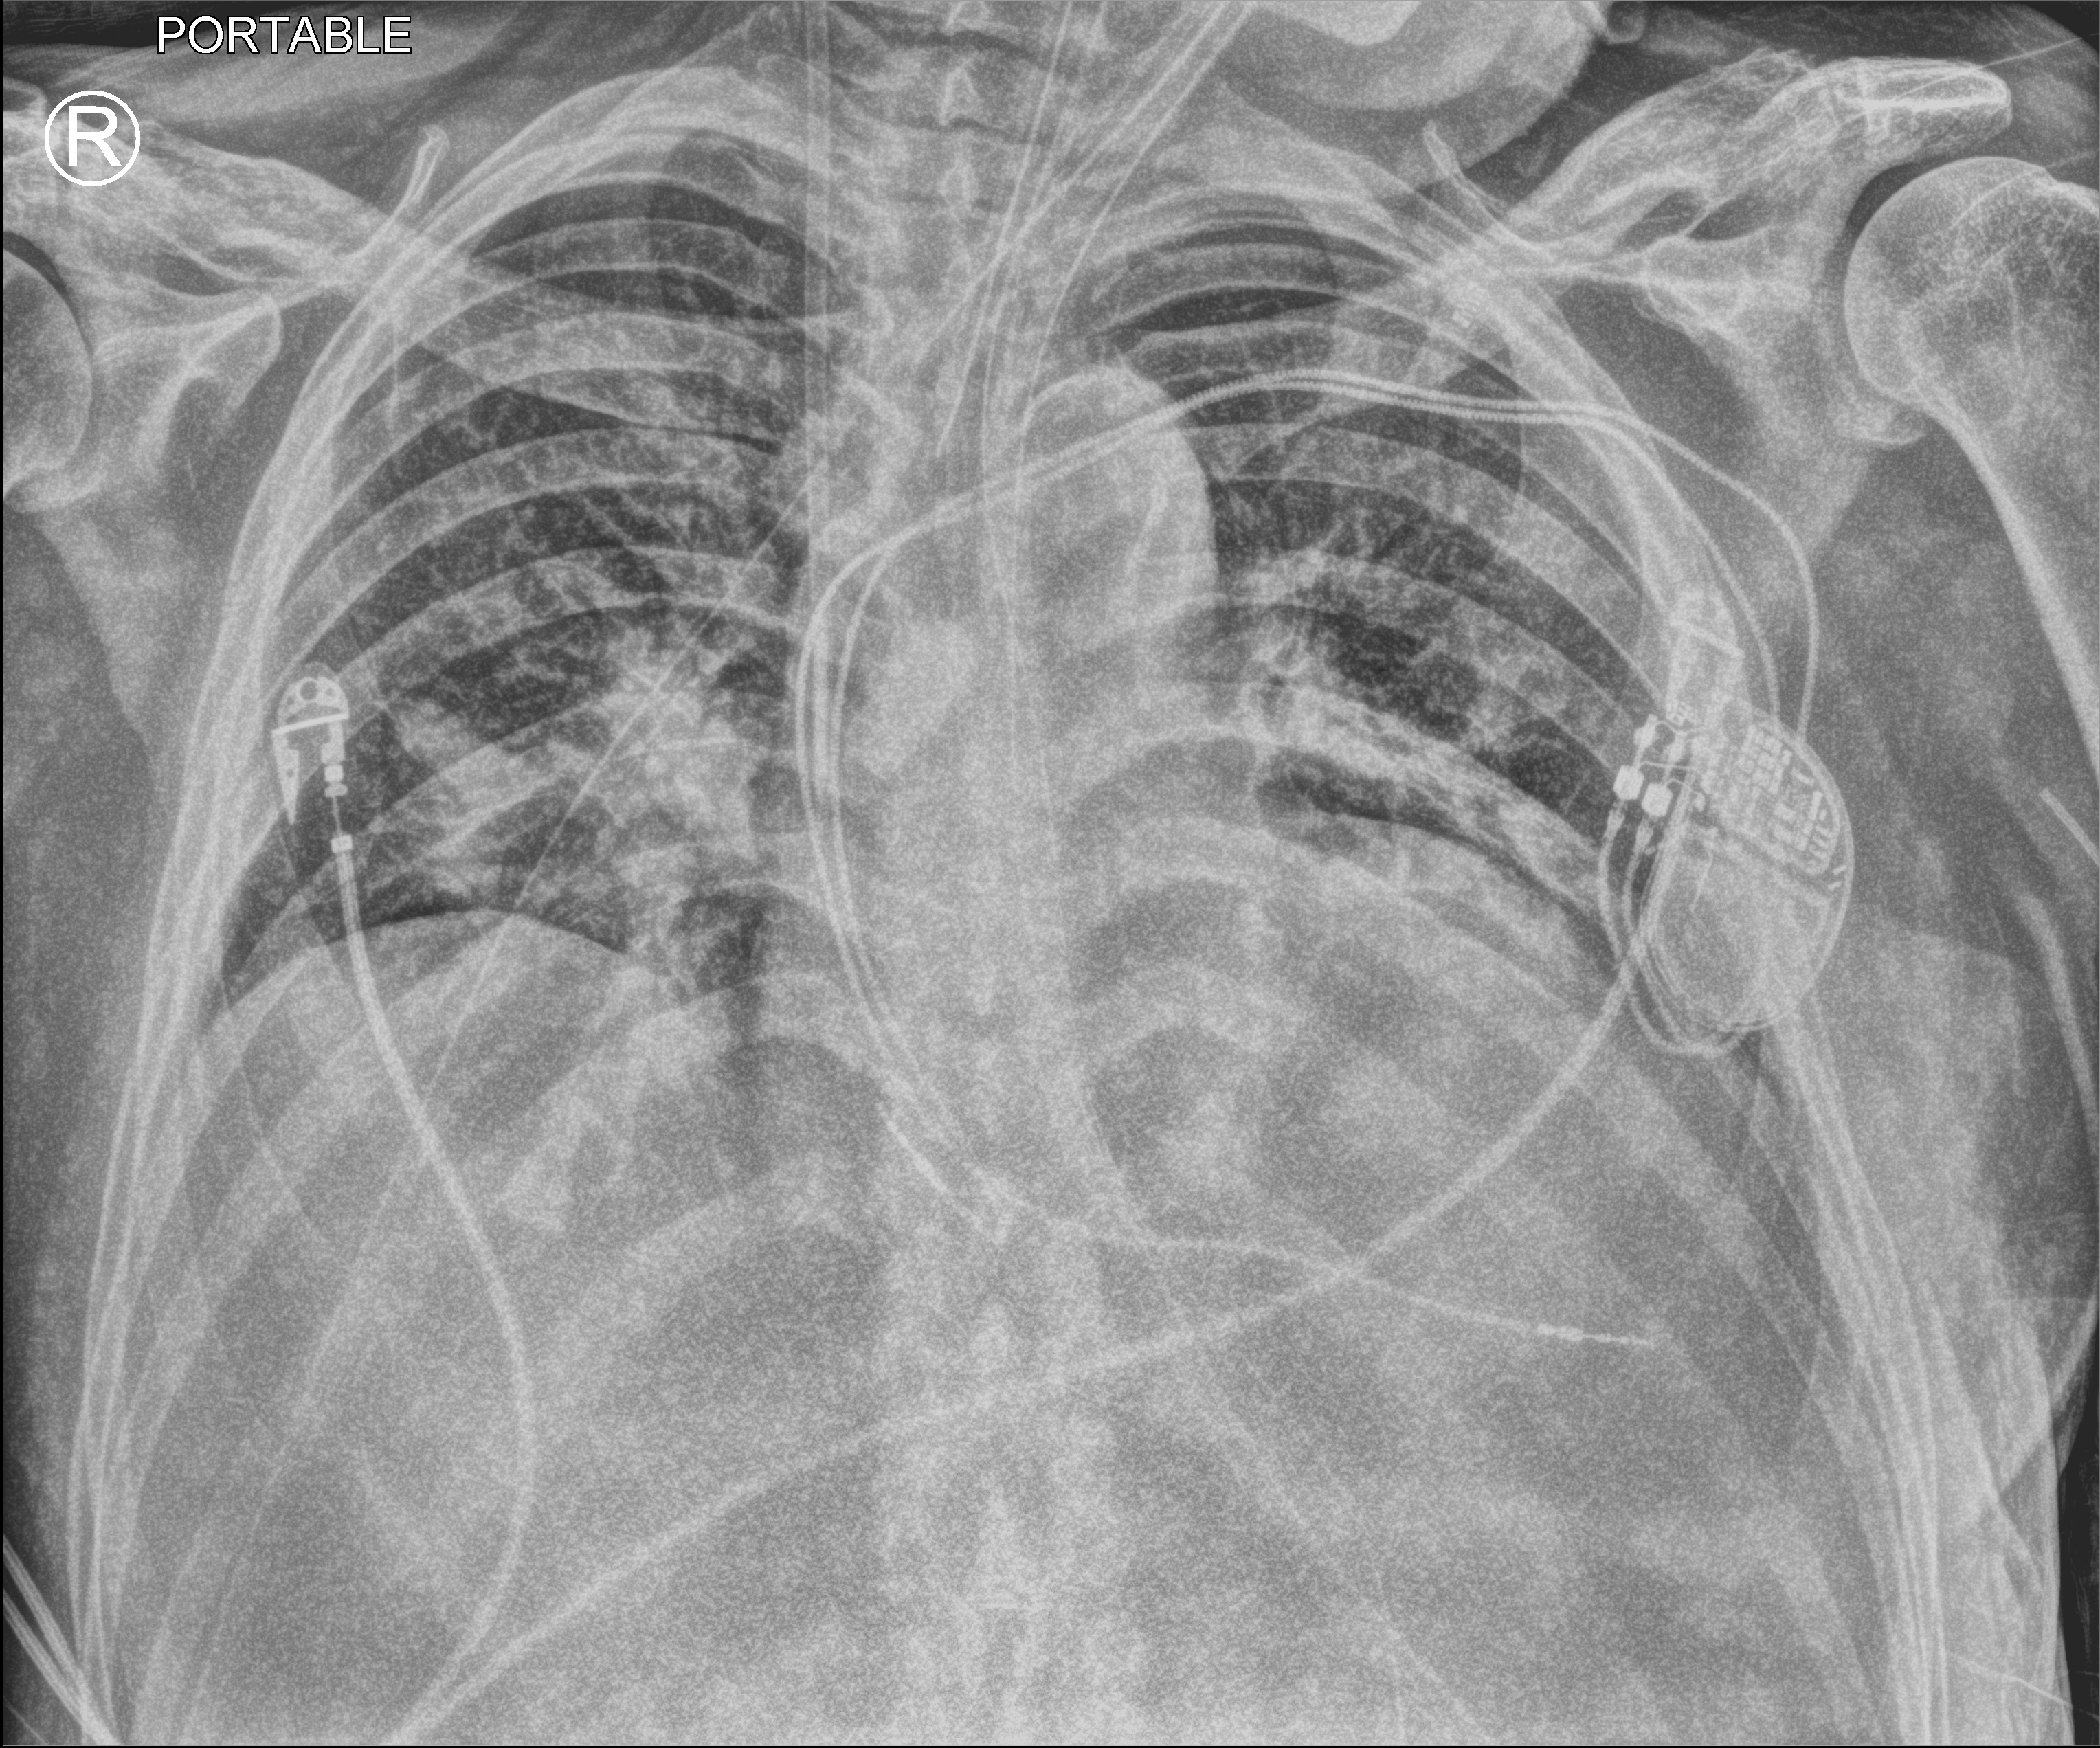
Bedside chest radiograph (computed radiography). Male patient hospitalised with COVID-19, age 60–74 years.
Hospital-stay facts (about this admission, not read from this image; timing relative to this image not recorded): mechanically ventilated during this hospital stay: yes; admitted to intensive care during this hospital stay: yes; length of hospital stay: 41 days.